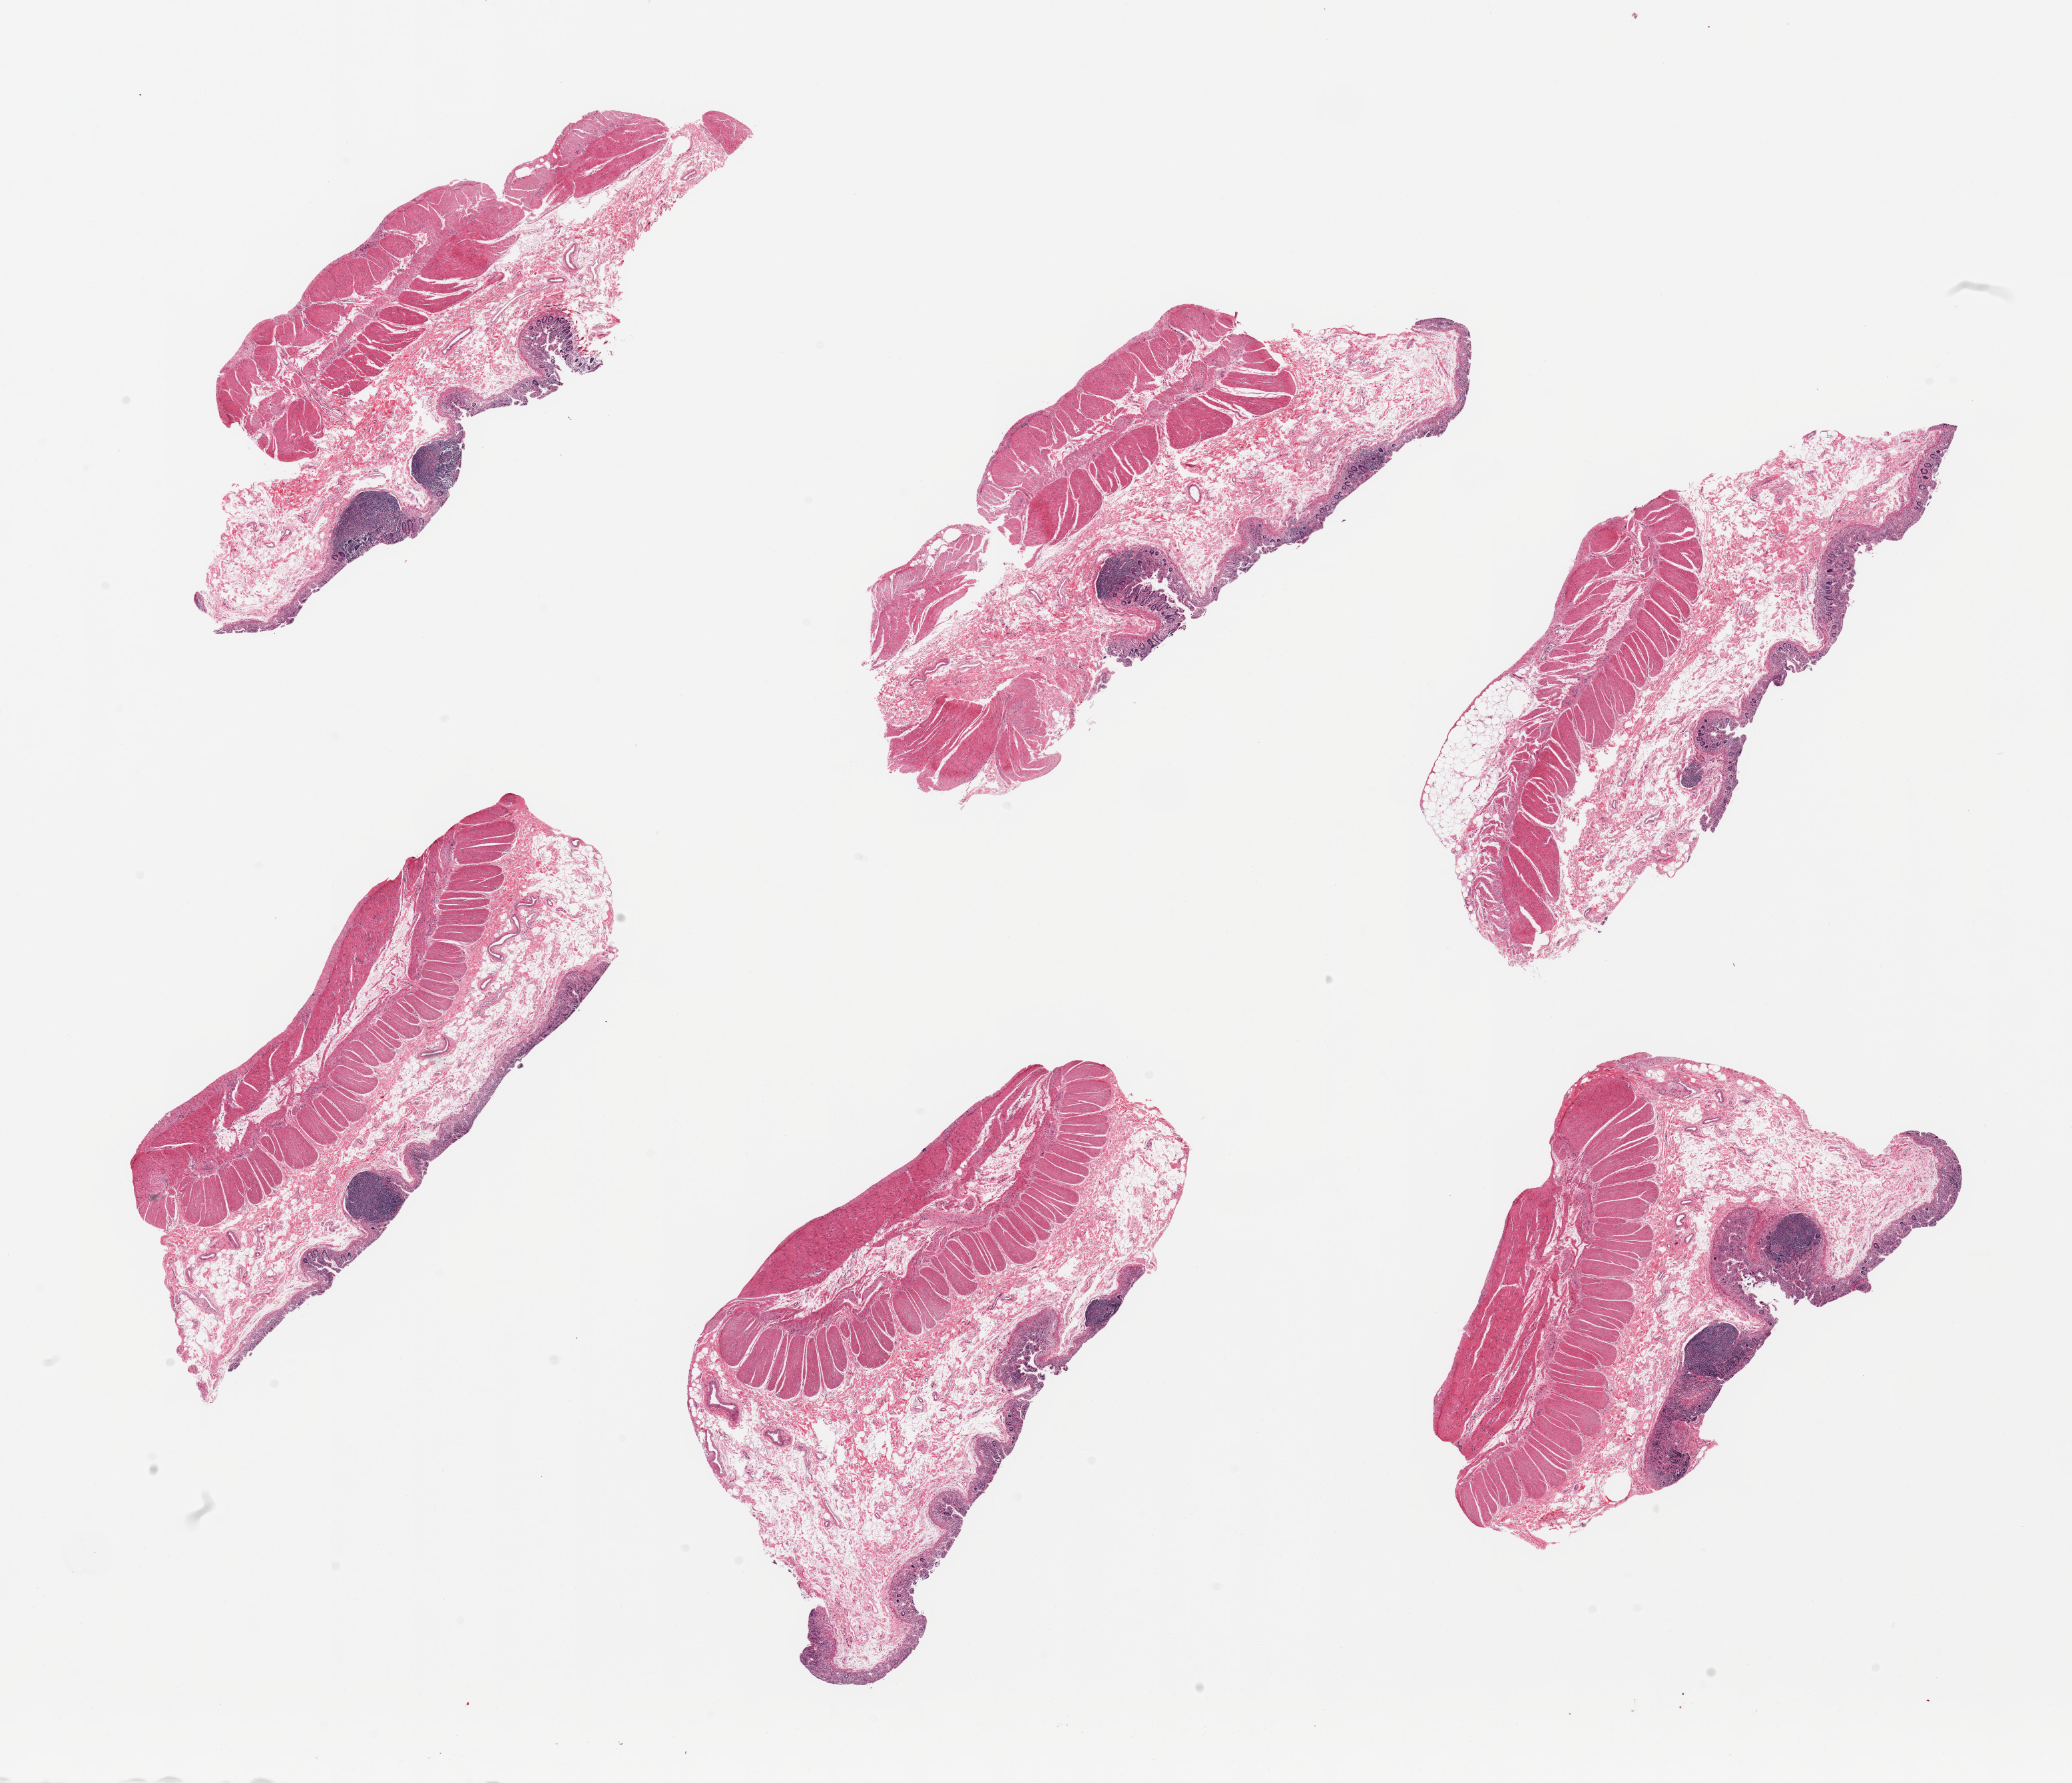
Digitized haematoxylin and eosin-stained section, a low-resolution overview of the entire scanned area, about 24.6 x 21.2 mm (slide scanned at 20x); PAXgene-fixed, paraffin-embedded tissue; section of ileum (target tissue); tissue donor sample. Donor sex: male.
Reviewer comment on this tissue sample: 6 pieces; each piece contains one to two well preserved lymphoid nodules; surface mucosa autolyzed and only focally preserved; muscle (not target) present on all.